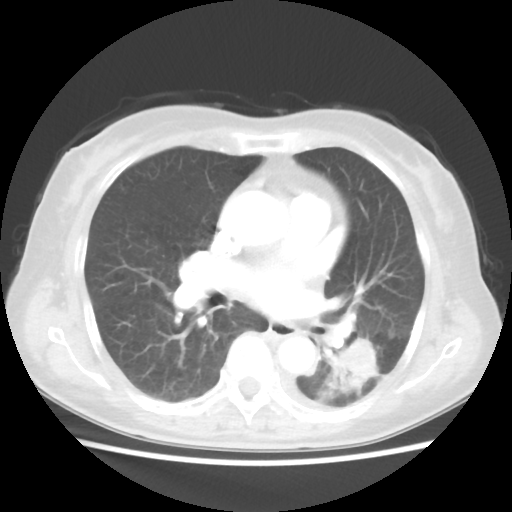
Chest CT, one axial slice. Slice 19 of 40 in the series (ordered by position). Reconstruction kernel STANDARD. 100 kVp. Lung window (W 1500 / L -600 HU). 5 mm slice thickness. 512 × 512 image matrix. Patient: female, 69 years. From the clinical record (not read from this slice): clinical TNM (as recorded): T1c N0 M0.
Outlined on this slice (bounding box drawn by a radiologist):
- lung tumour (recorded histology: adenocarcinoma): bounding box [x1, y1, x2, y2] px = [330, 333, 381, 397]